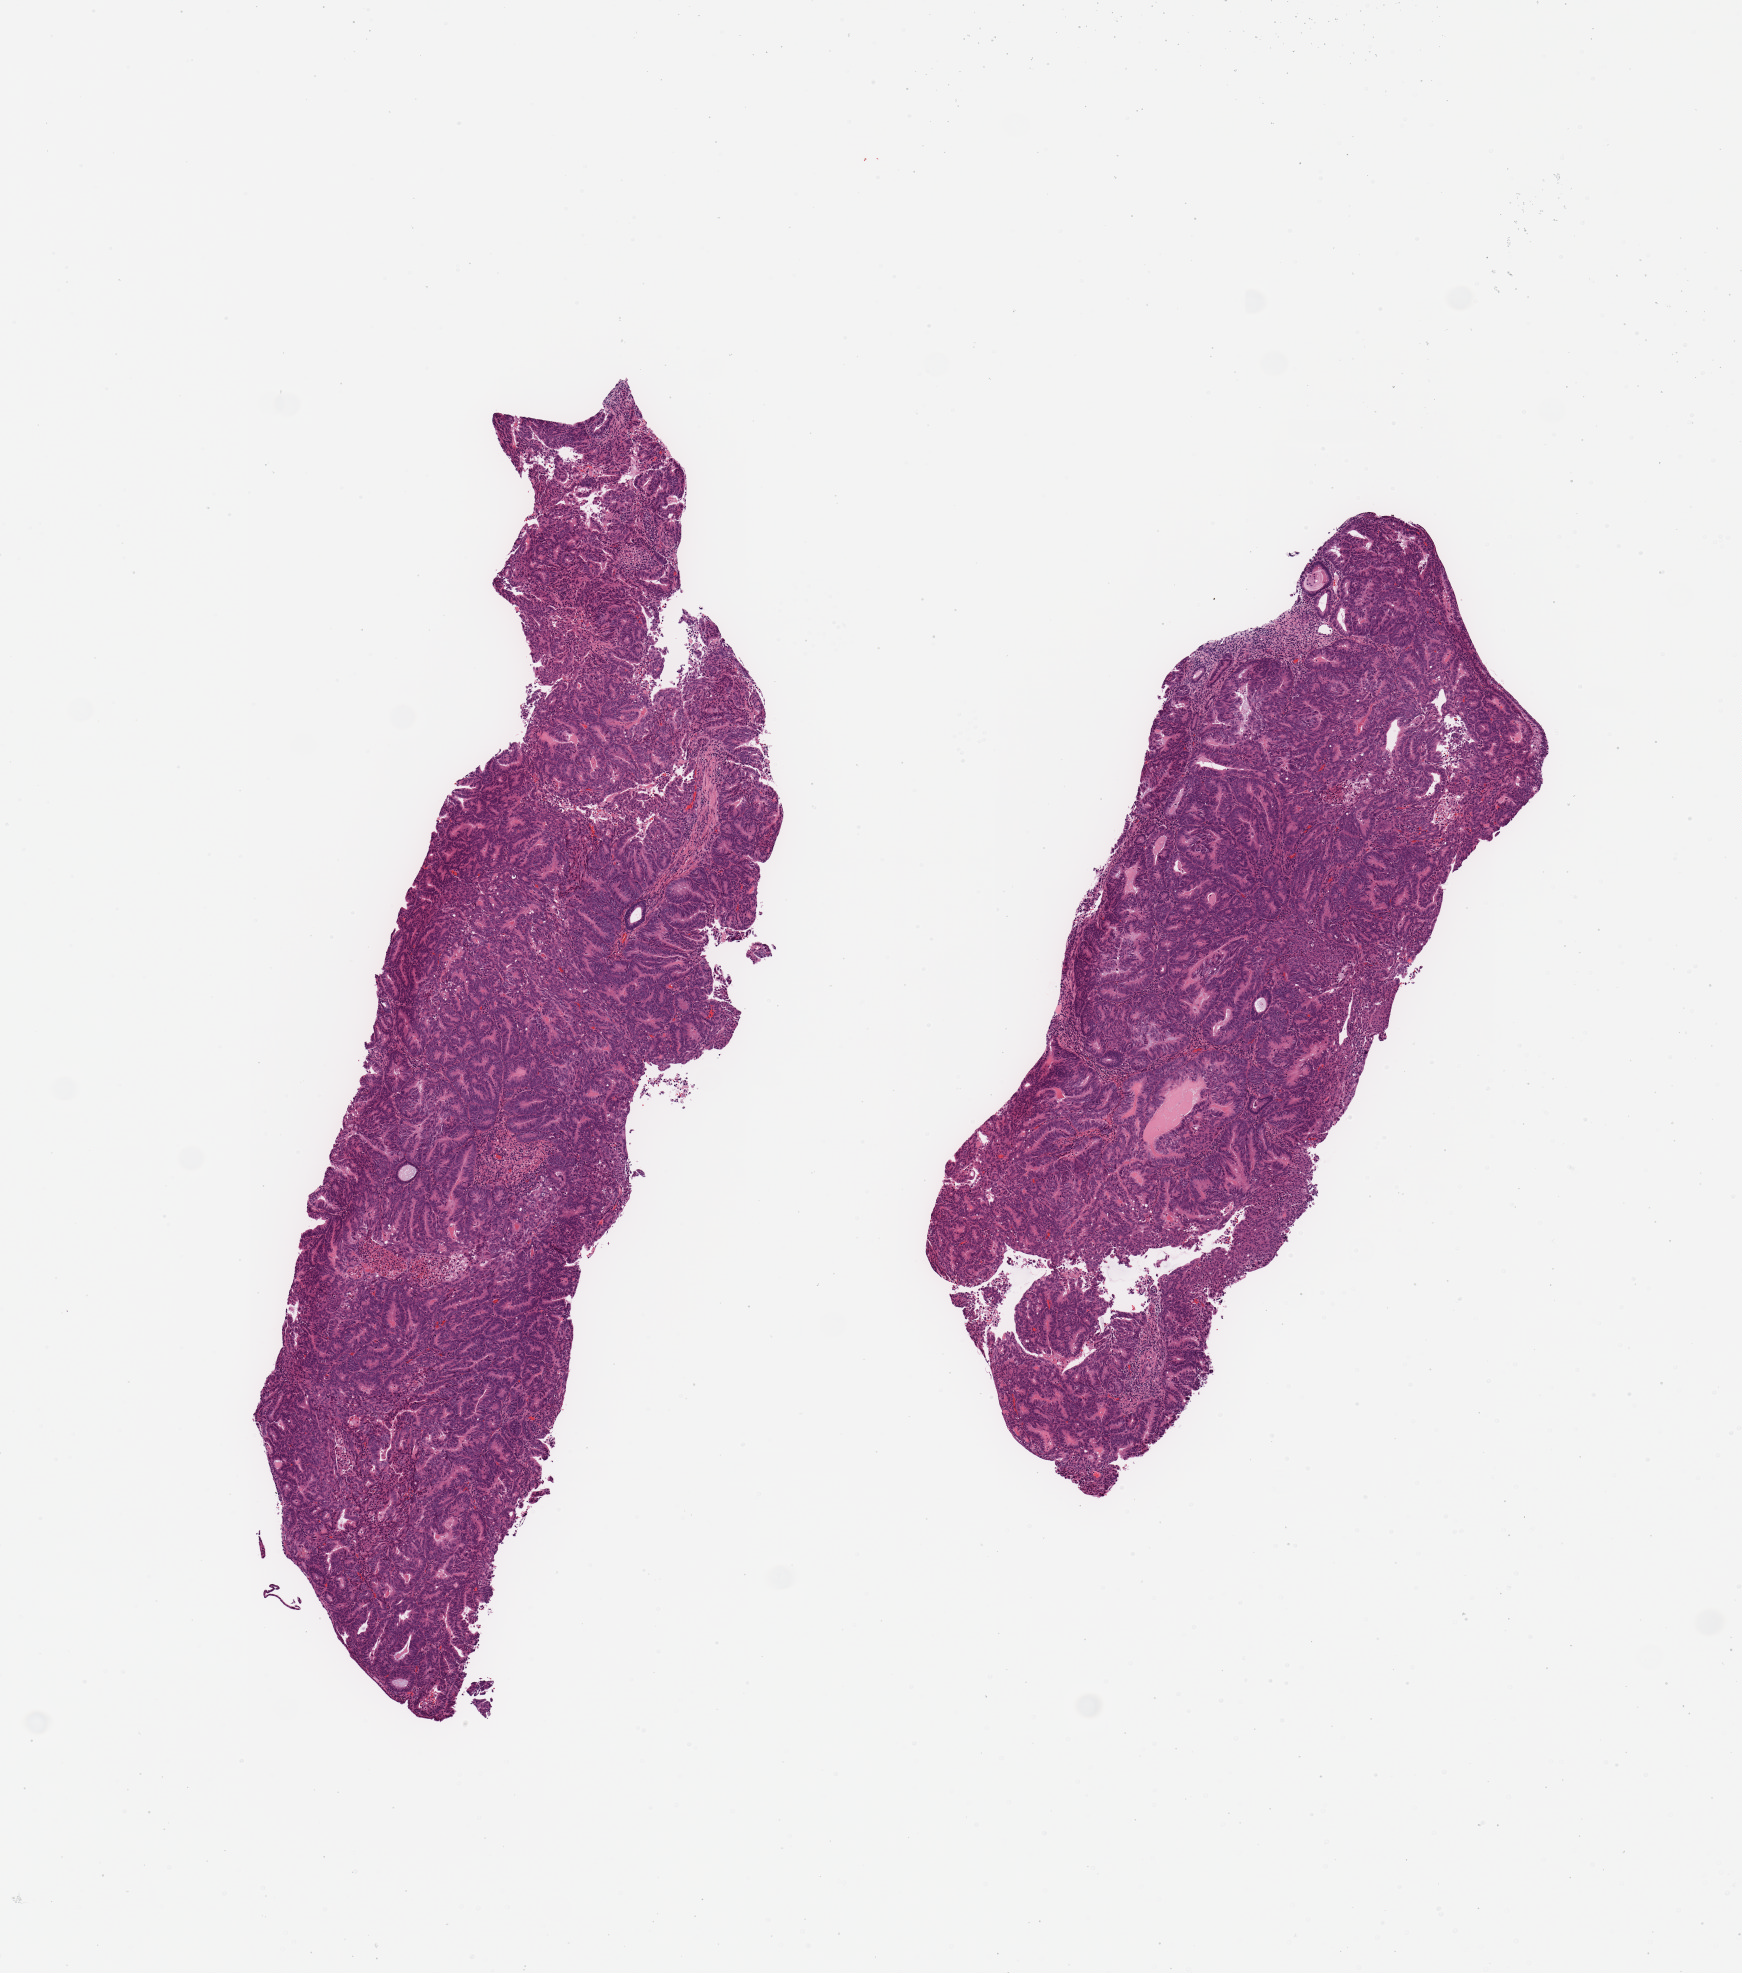
Hematoxylin and eosin (H&E) stained whole-slide image — low-resolution overview of the scanned area, about 6.9 x 7.8 mm (slide scanned at 20x), tumour tissue sample, uterus. Female, 50 y/o.
Histologic diagnosis: Endometrioid adenocarcinoma, NOS.